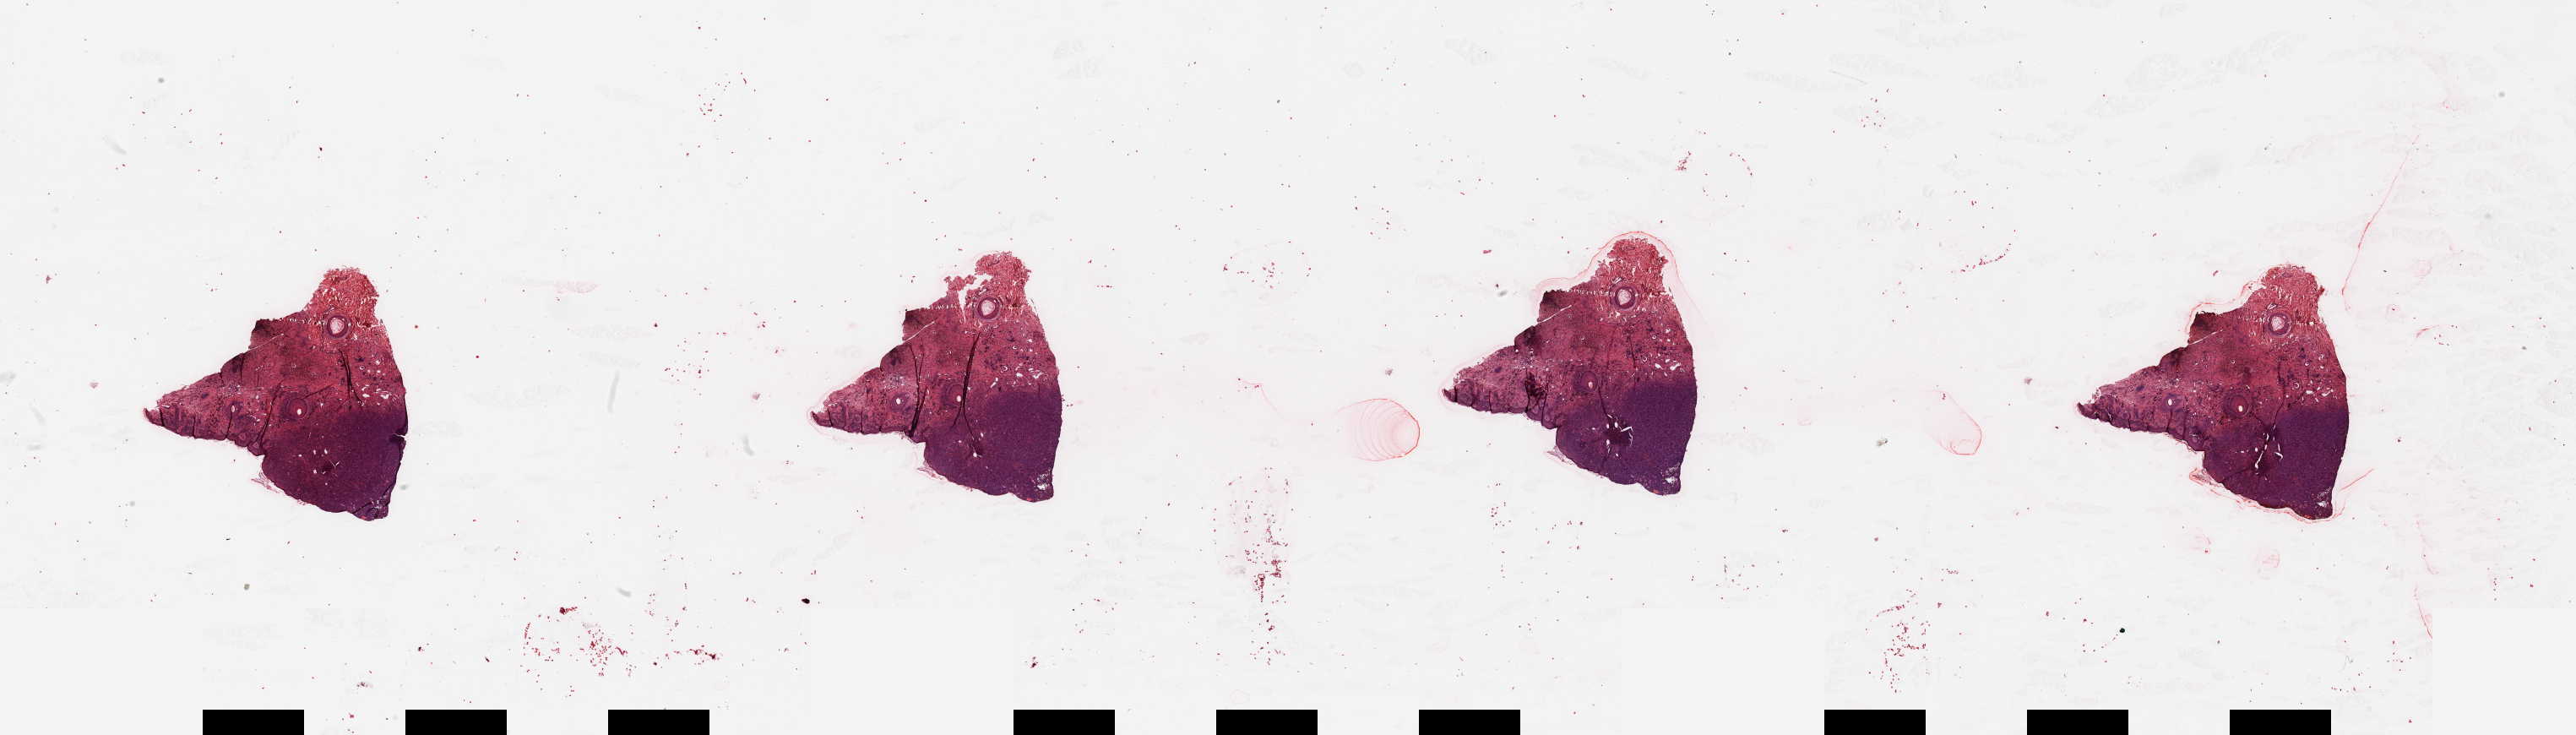
Whole-slide histology image, H&E — a low-resolution overview of the entire scanned area, about 48.2 x 13.8 mm, tumour tissue sample, sampled site: trunk. 69-year-old male patient. Composition of this section per pathologist review: tumour nuclei 90%, necrosis 0%.
Histologic diagnosis: Malignant melanoma, NOS.